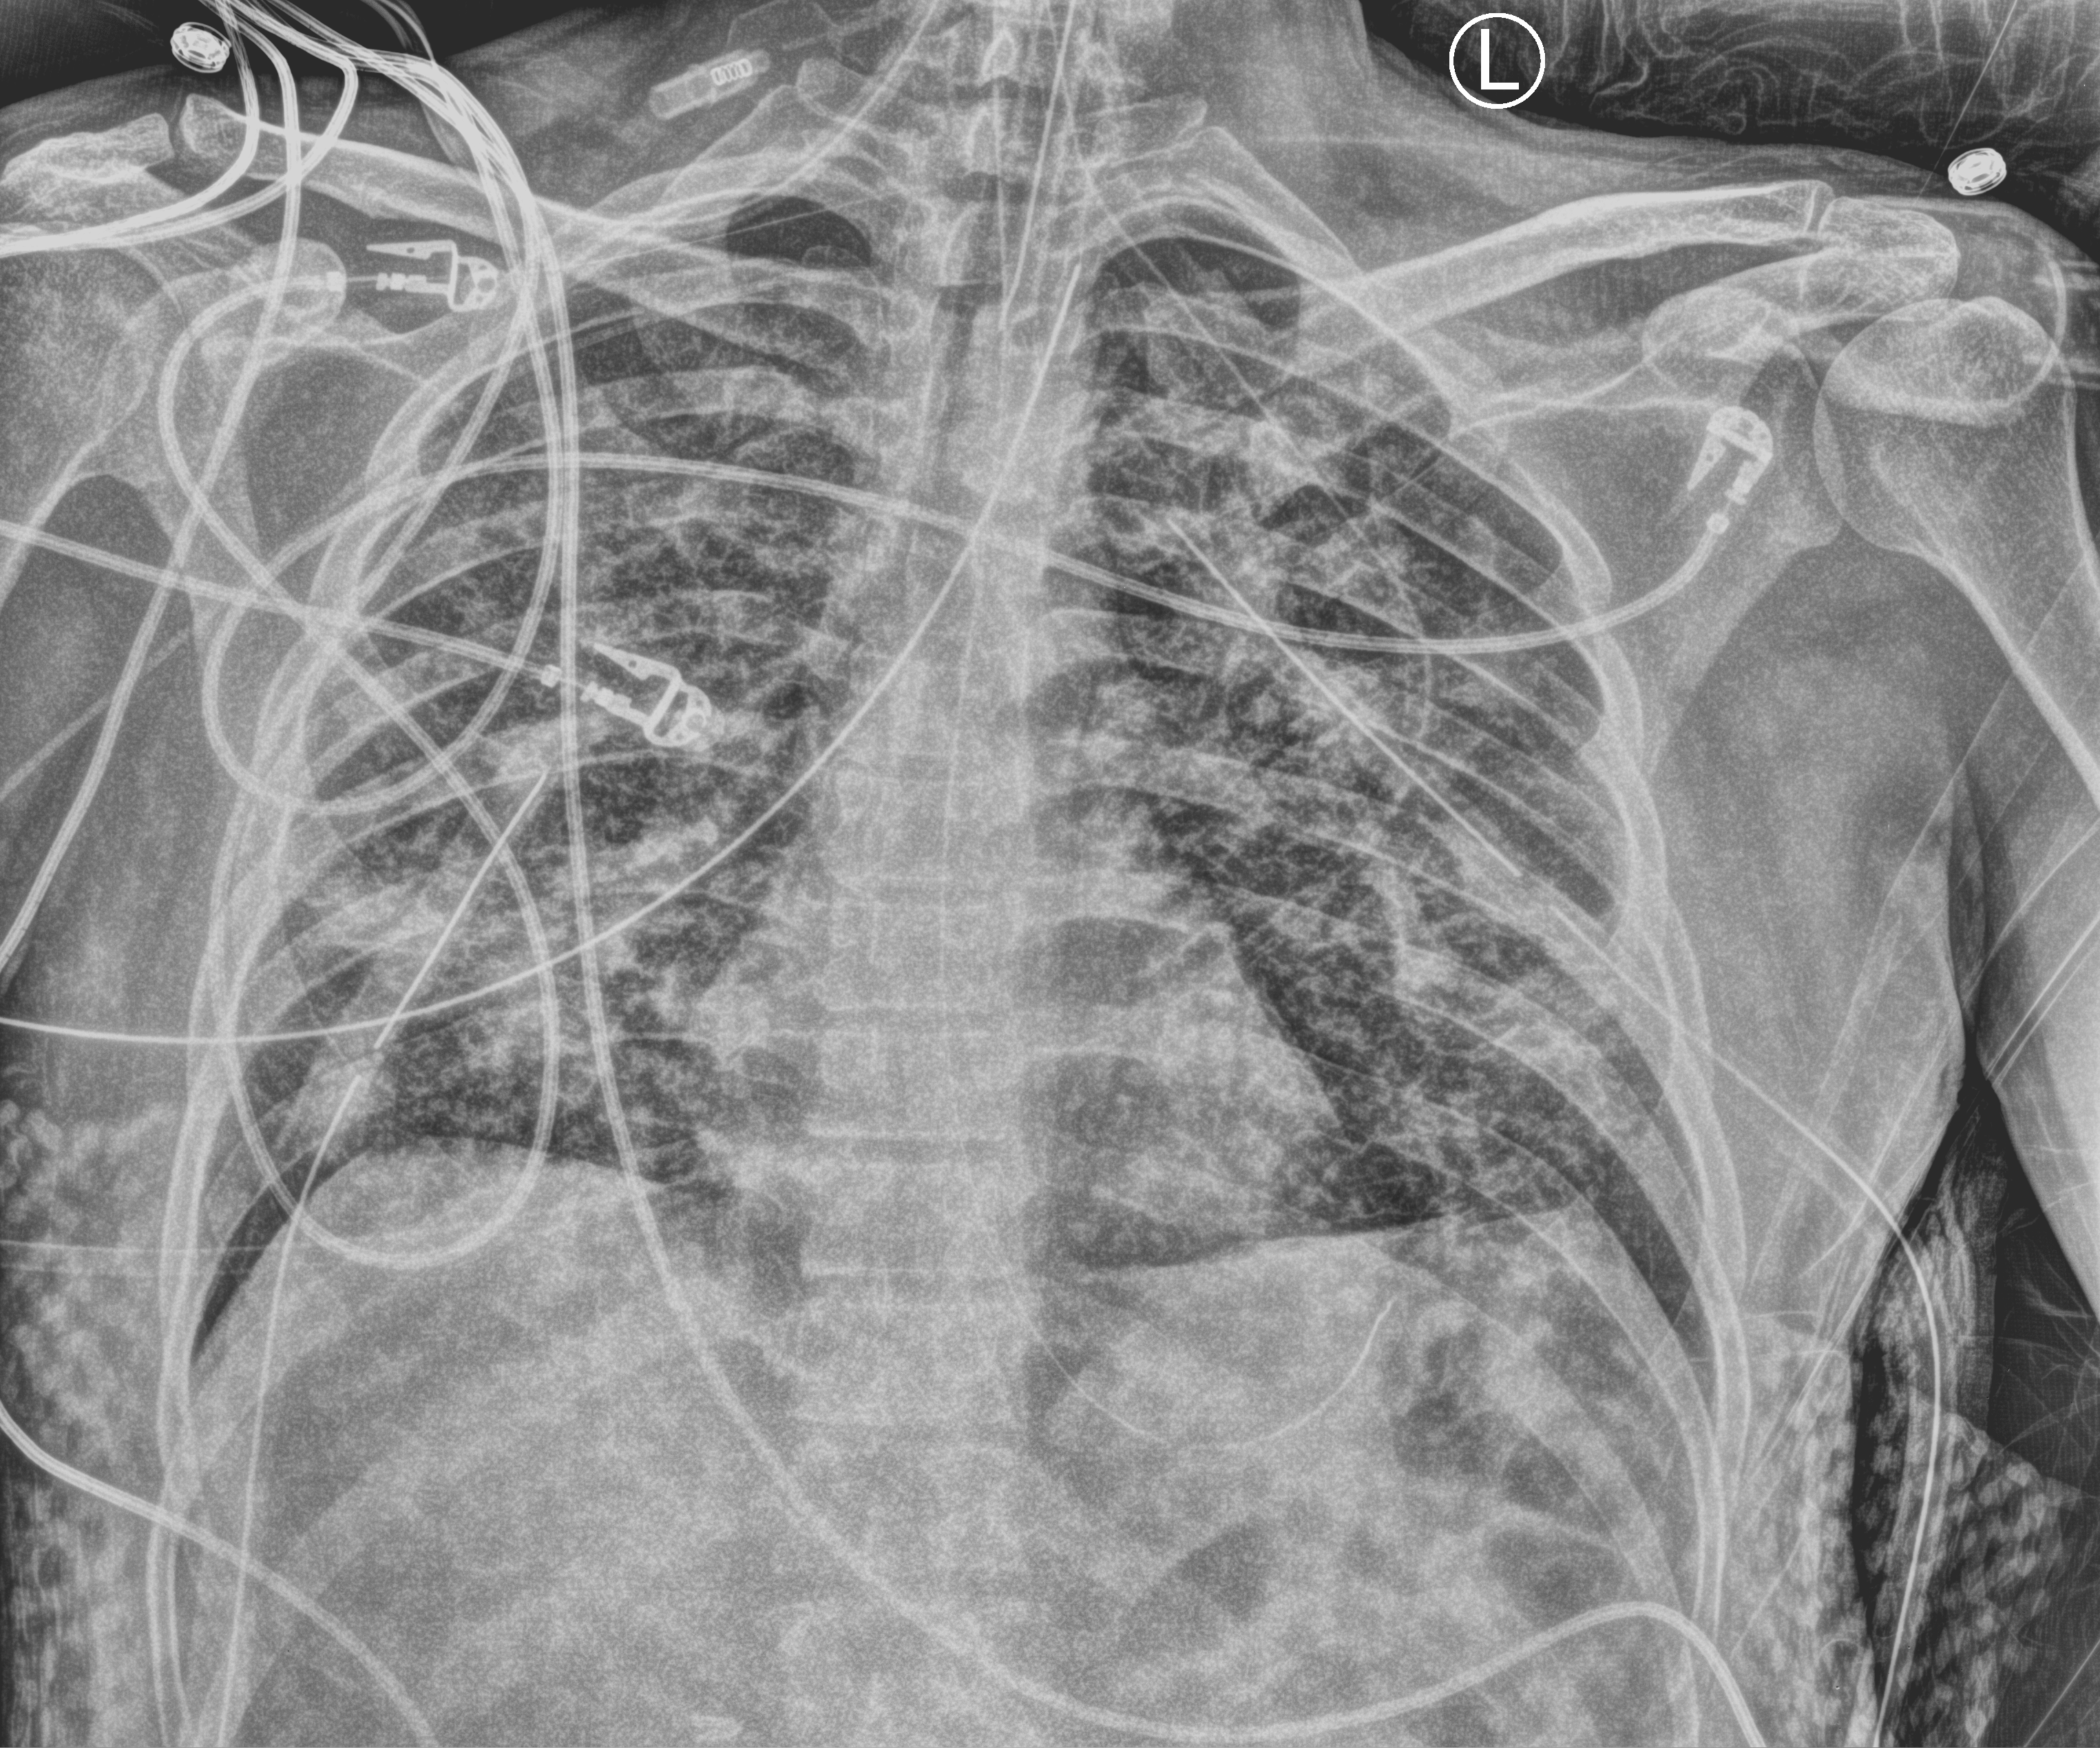
Portable chest radiograph, anteroposterior (AP) projection. Male patient hospitalised with COVID-19, age 18–59 years.
From the hospital-stay record, not from the radiograph (when in the stay this image was taken is not recorded):
- admitted to intensive care during this hospital stay: yes
- hypertension (admission record): no